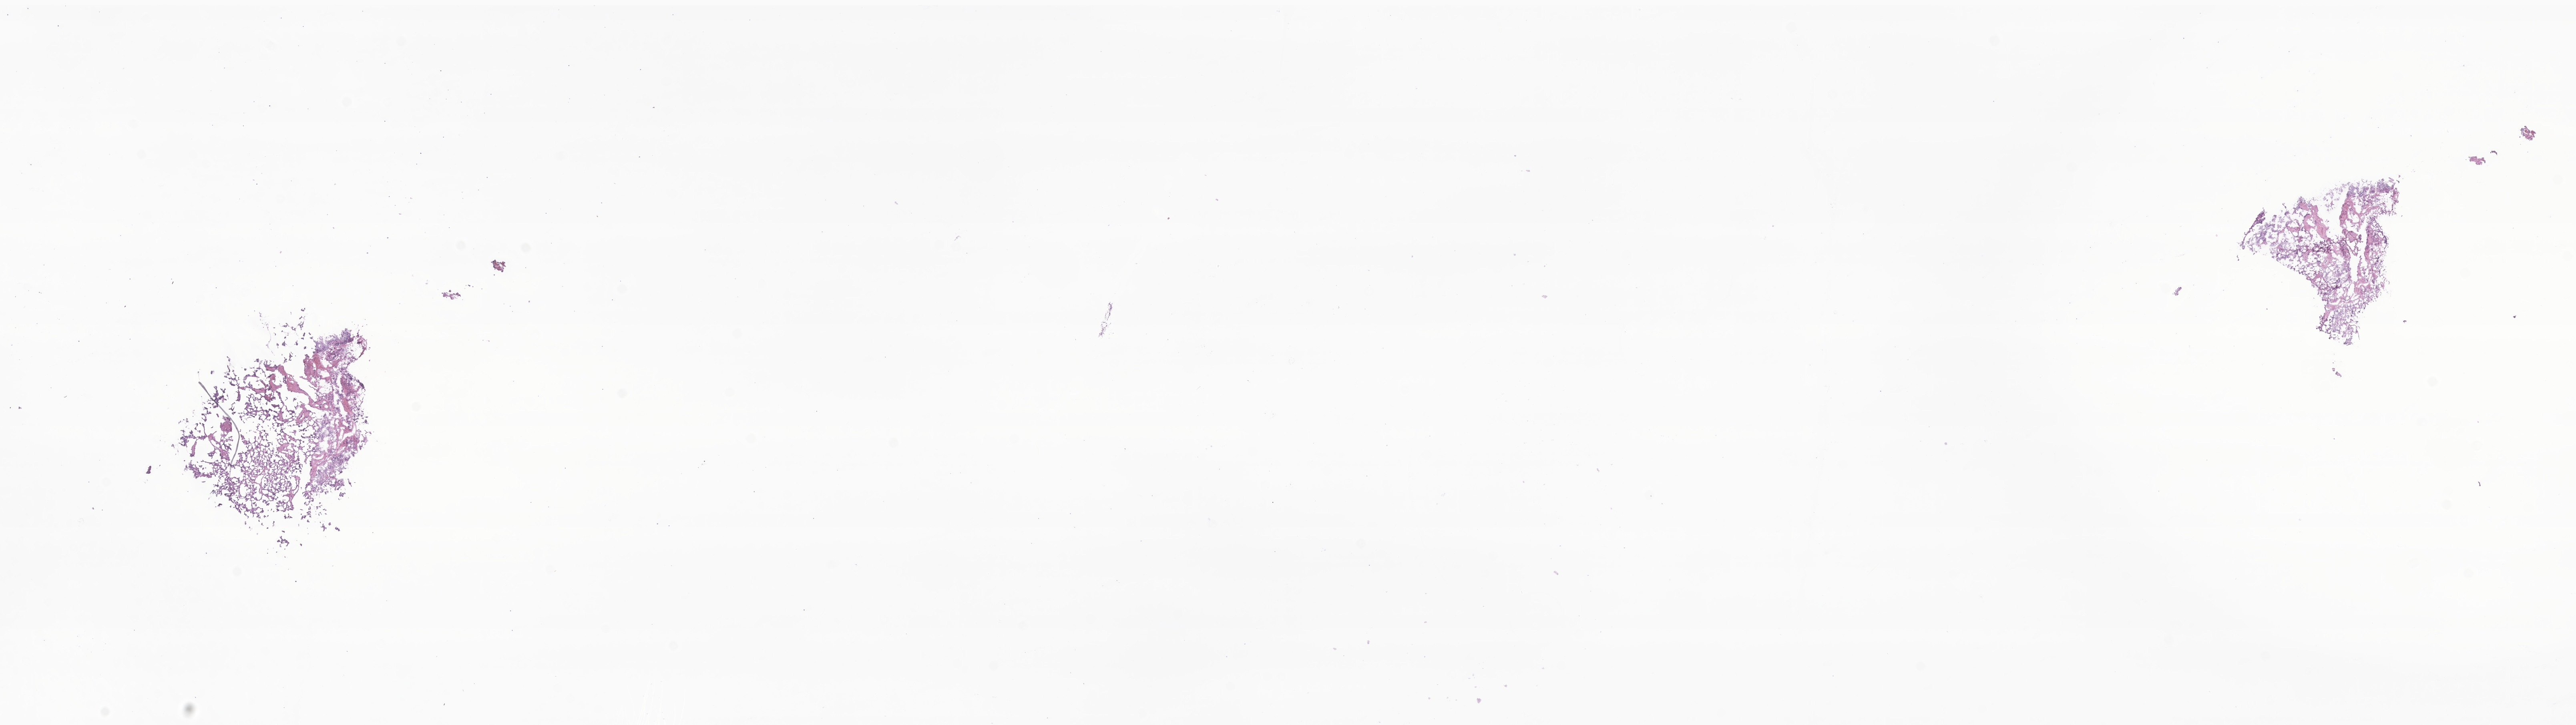
Digitized H&E-stained section of tumor tissue from the cerebellum — whole scanned area (about 27.1 x 7.6 mm) shown as a low-resolution overview. Cryosection (OCT / tissue freezing medium). Patient: female, age 60 months (5 years).
Diagnosis: Medulloblastoma, NOS.